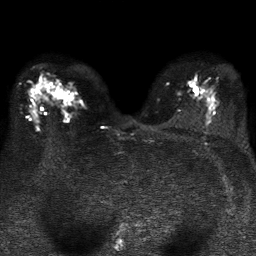
Breast MRI, one axial slice. Slice 23 of 37 in the series (ordered by position). Diffusion-weighted series; image 2 of 4 stored at this slice position (different b-values; order by instance number). 1.5 T. 256 × 256 image matrix. Female patient.
Annotated regions visible in this slice (expert manual segmentation):
- tumour on diffusion-weighted imaging: bounding box <55,86,63,97> (left, top, right, bottom; pixels)